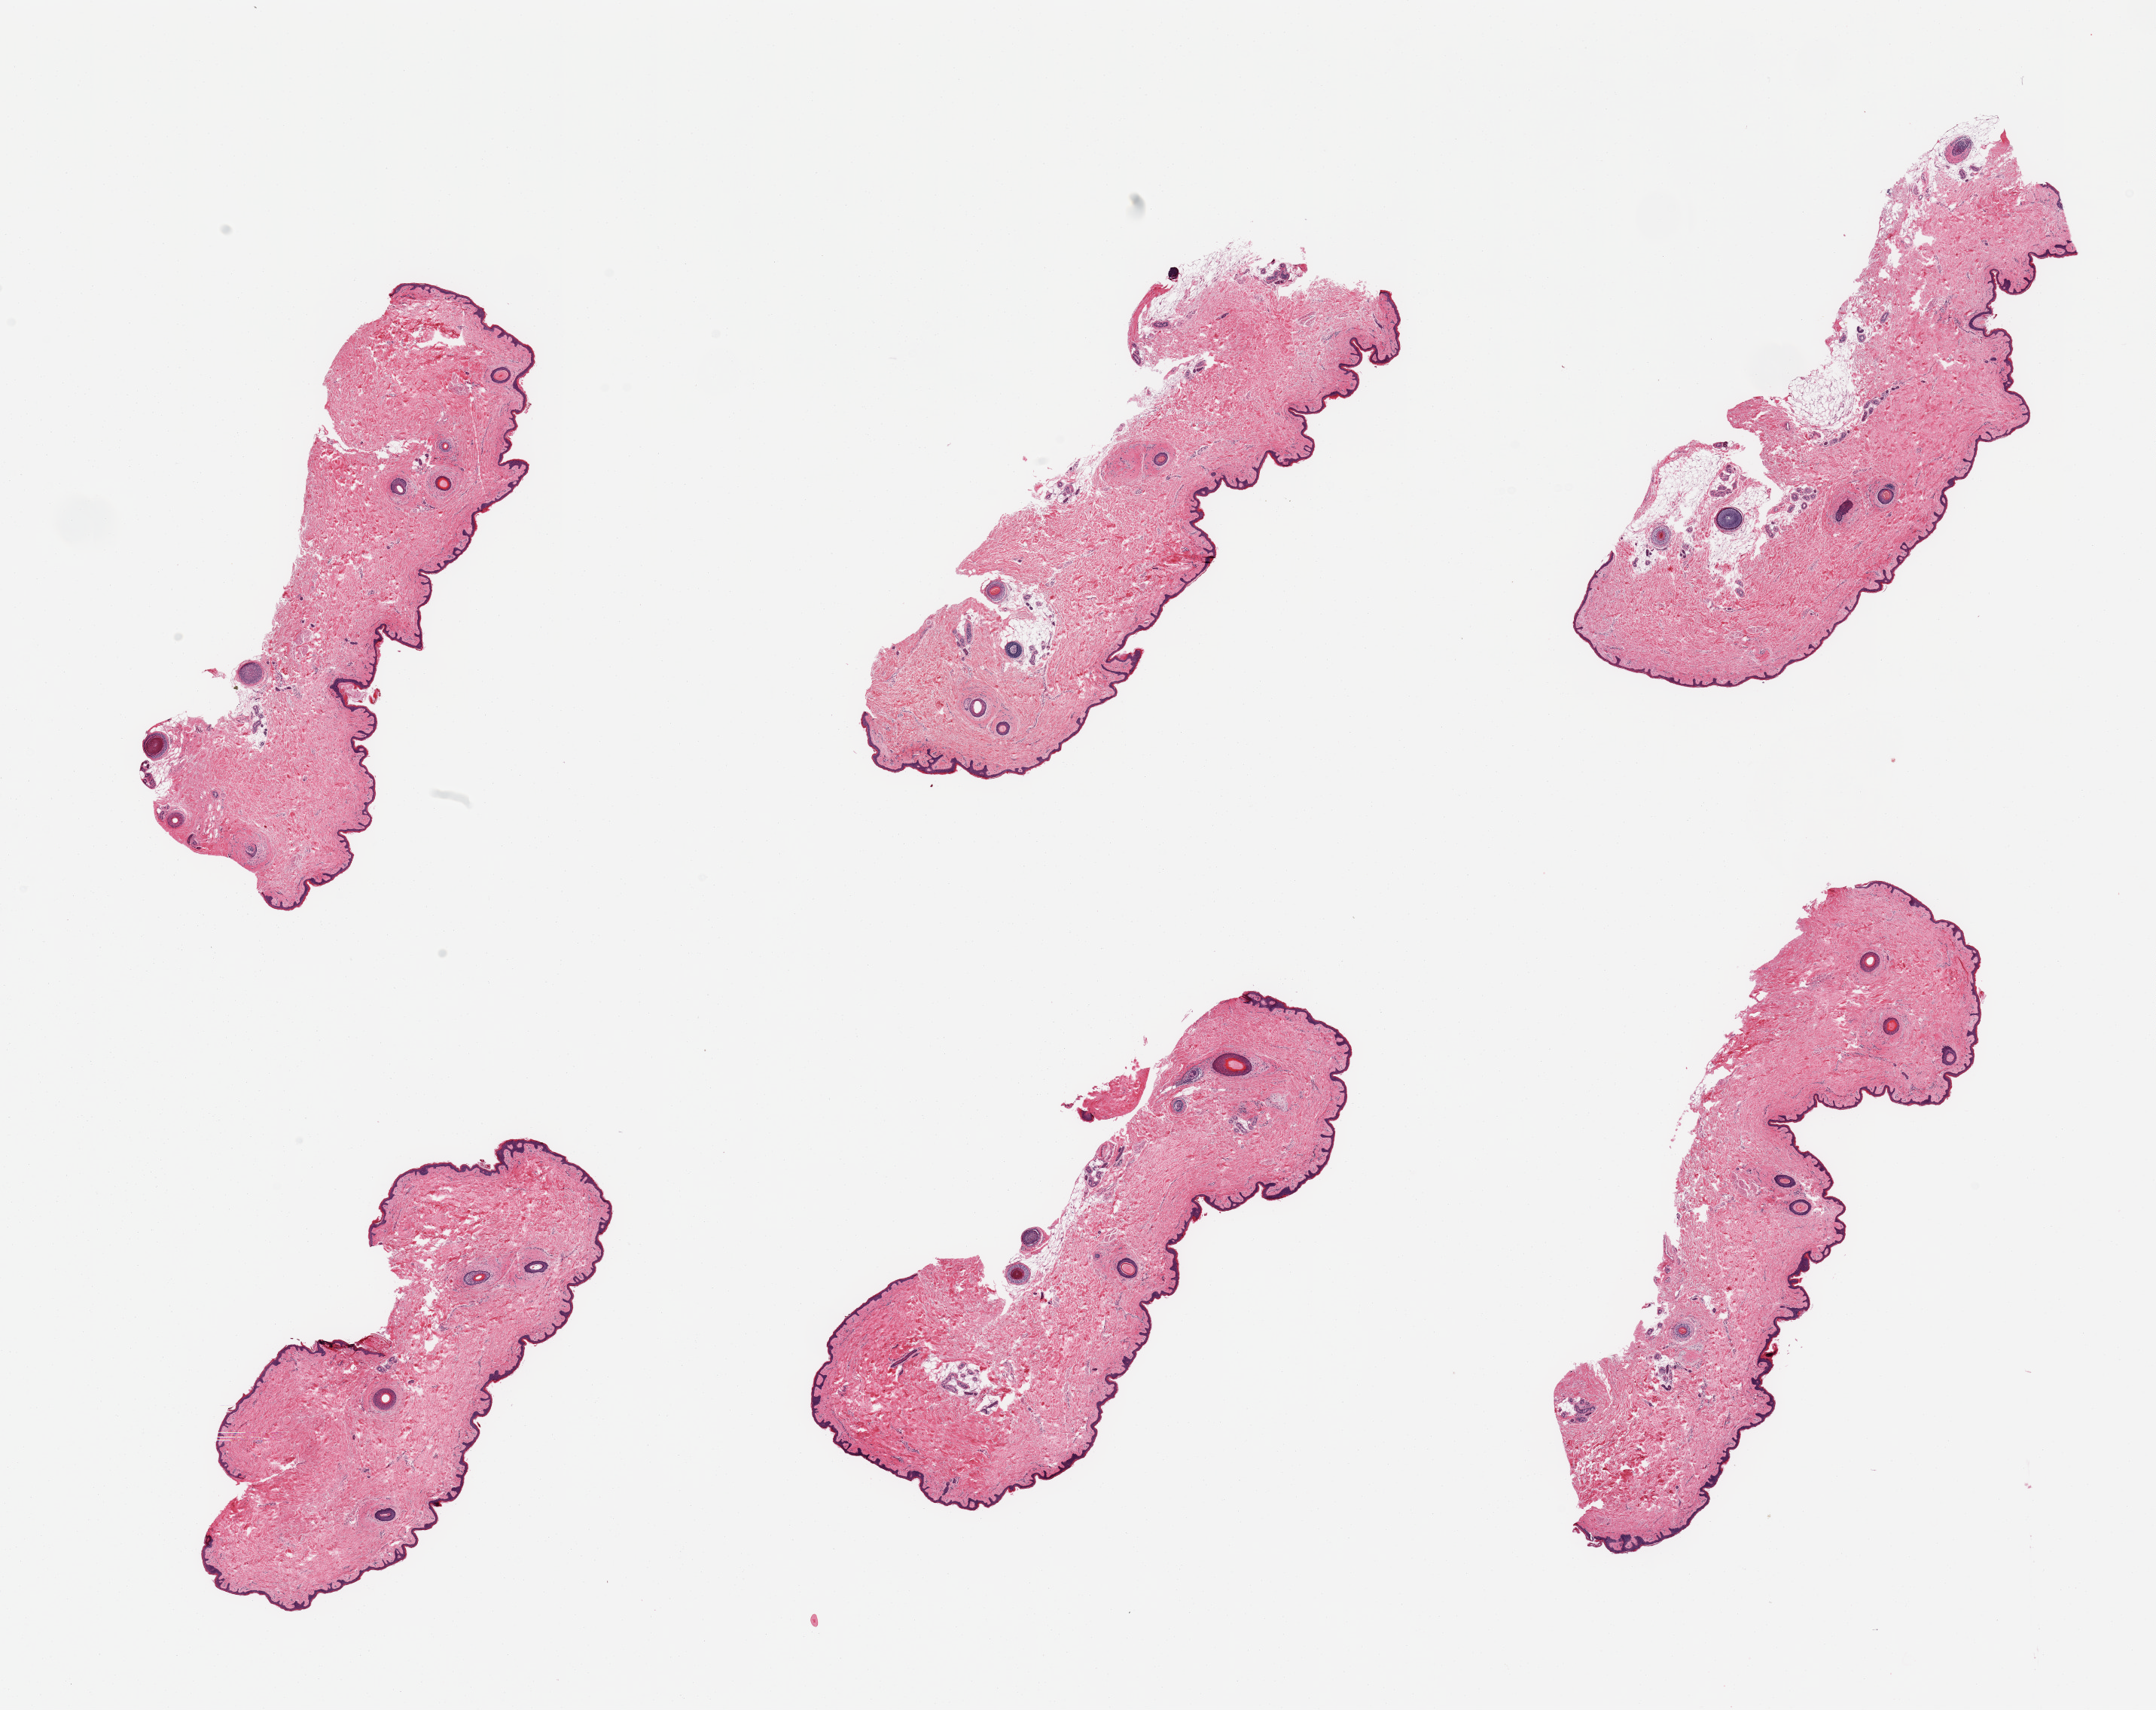
Digitized H&E-stained section, shown as a low-resolution overview of the whole scanned area (about 22.6 x 18.0 mm, acquisition: 20x scan); PAXgene-fixed, paraffin-embedded tissue; section of skin of suprapubic region (target tissue); tissue donor sample. Donor sex: female.
Pathologist's review note for this sample: 6 pieces, minimal dermal fat; squamous epithelium is ~25 microns.